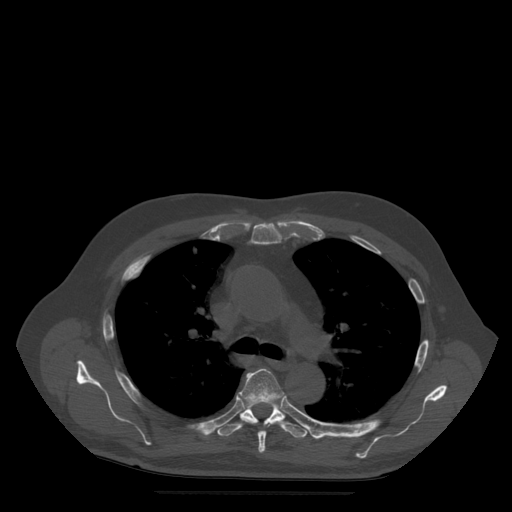
CT including the spine, one axial slice; slice 364 of 522 in the series (ordered by position); bone window (W 1800 / L 400 HU); 1.25 mm slice thickness; 512 × 512 image matrix. Patient age 72 years. From the clinical record (not read from this slice): primary cancer: prostate.
Annotated regions visible in this slice (semi-automatically segmented with operator editing):
- T5 vertebra: bounding box [x1, y1, x2, y2] px = [239, 369, 286, 453]
- T6 vertebra: [217, 376, 308, 438]